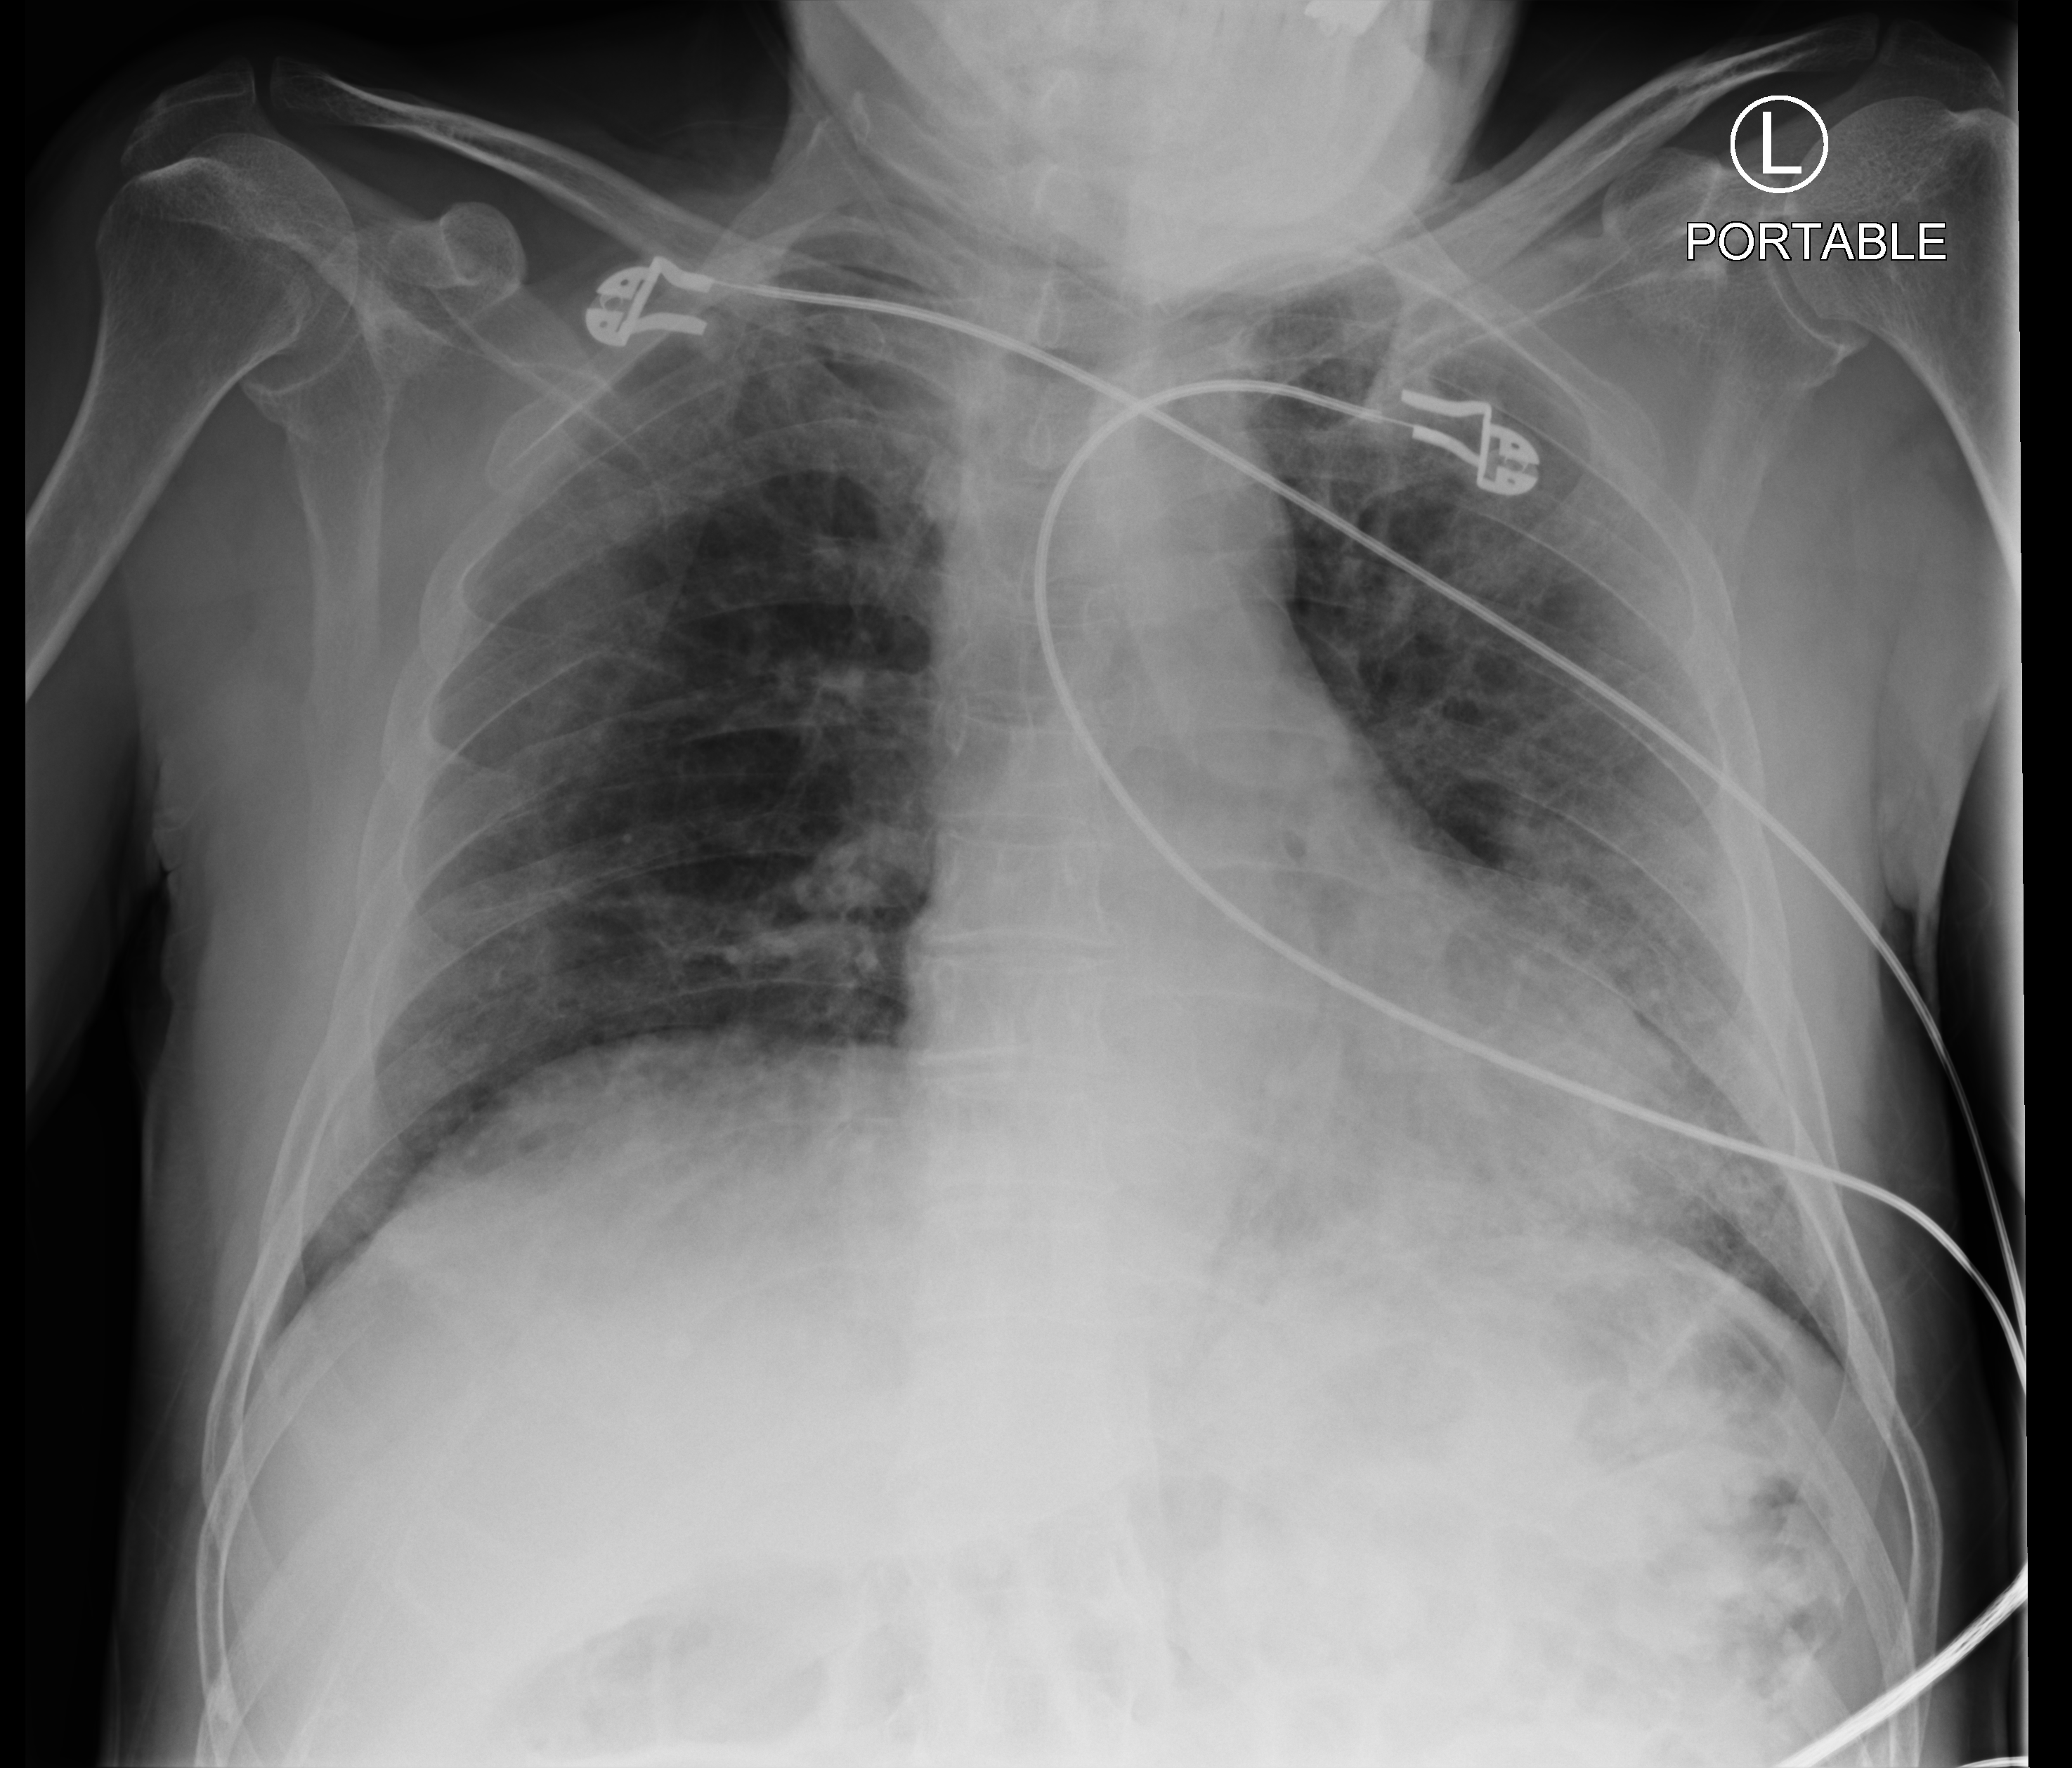
Chest X-ray (portable), anteroposterior (AP) projection. Patient hospitalised with COVID-19; male, aged 60–74 years.
Hospital-stay facts (about this admission, not read from this image; timing relative to this image not recorded):
- length of hospital stay: 10 days
- admitted to intensive care during this hospital stay: no